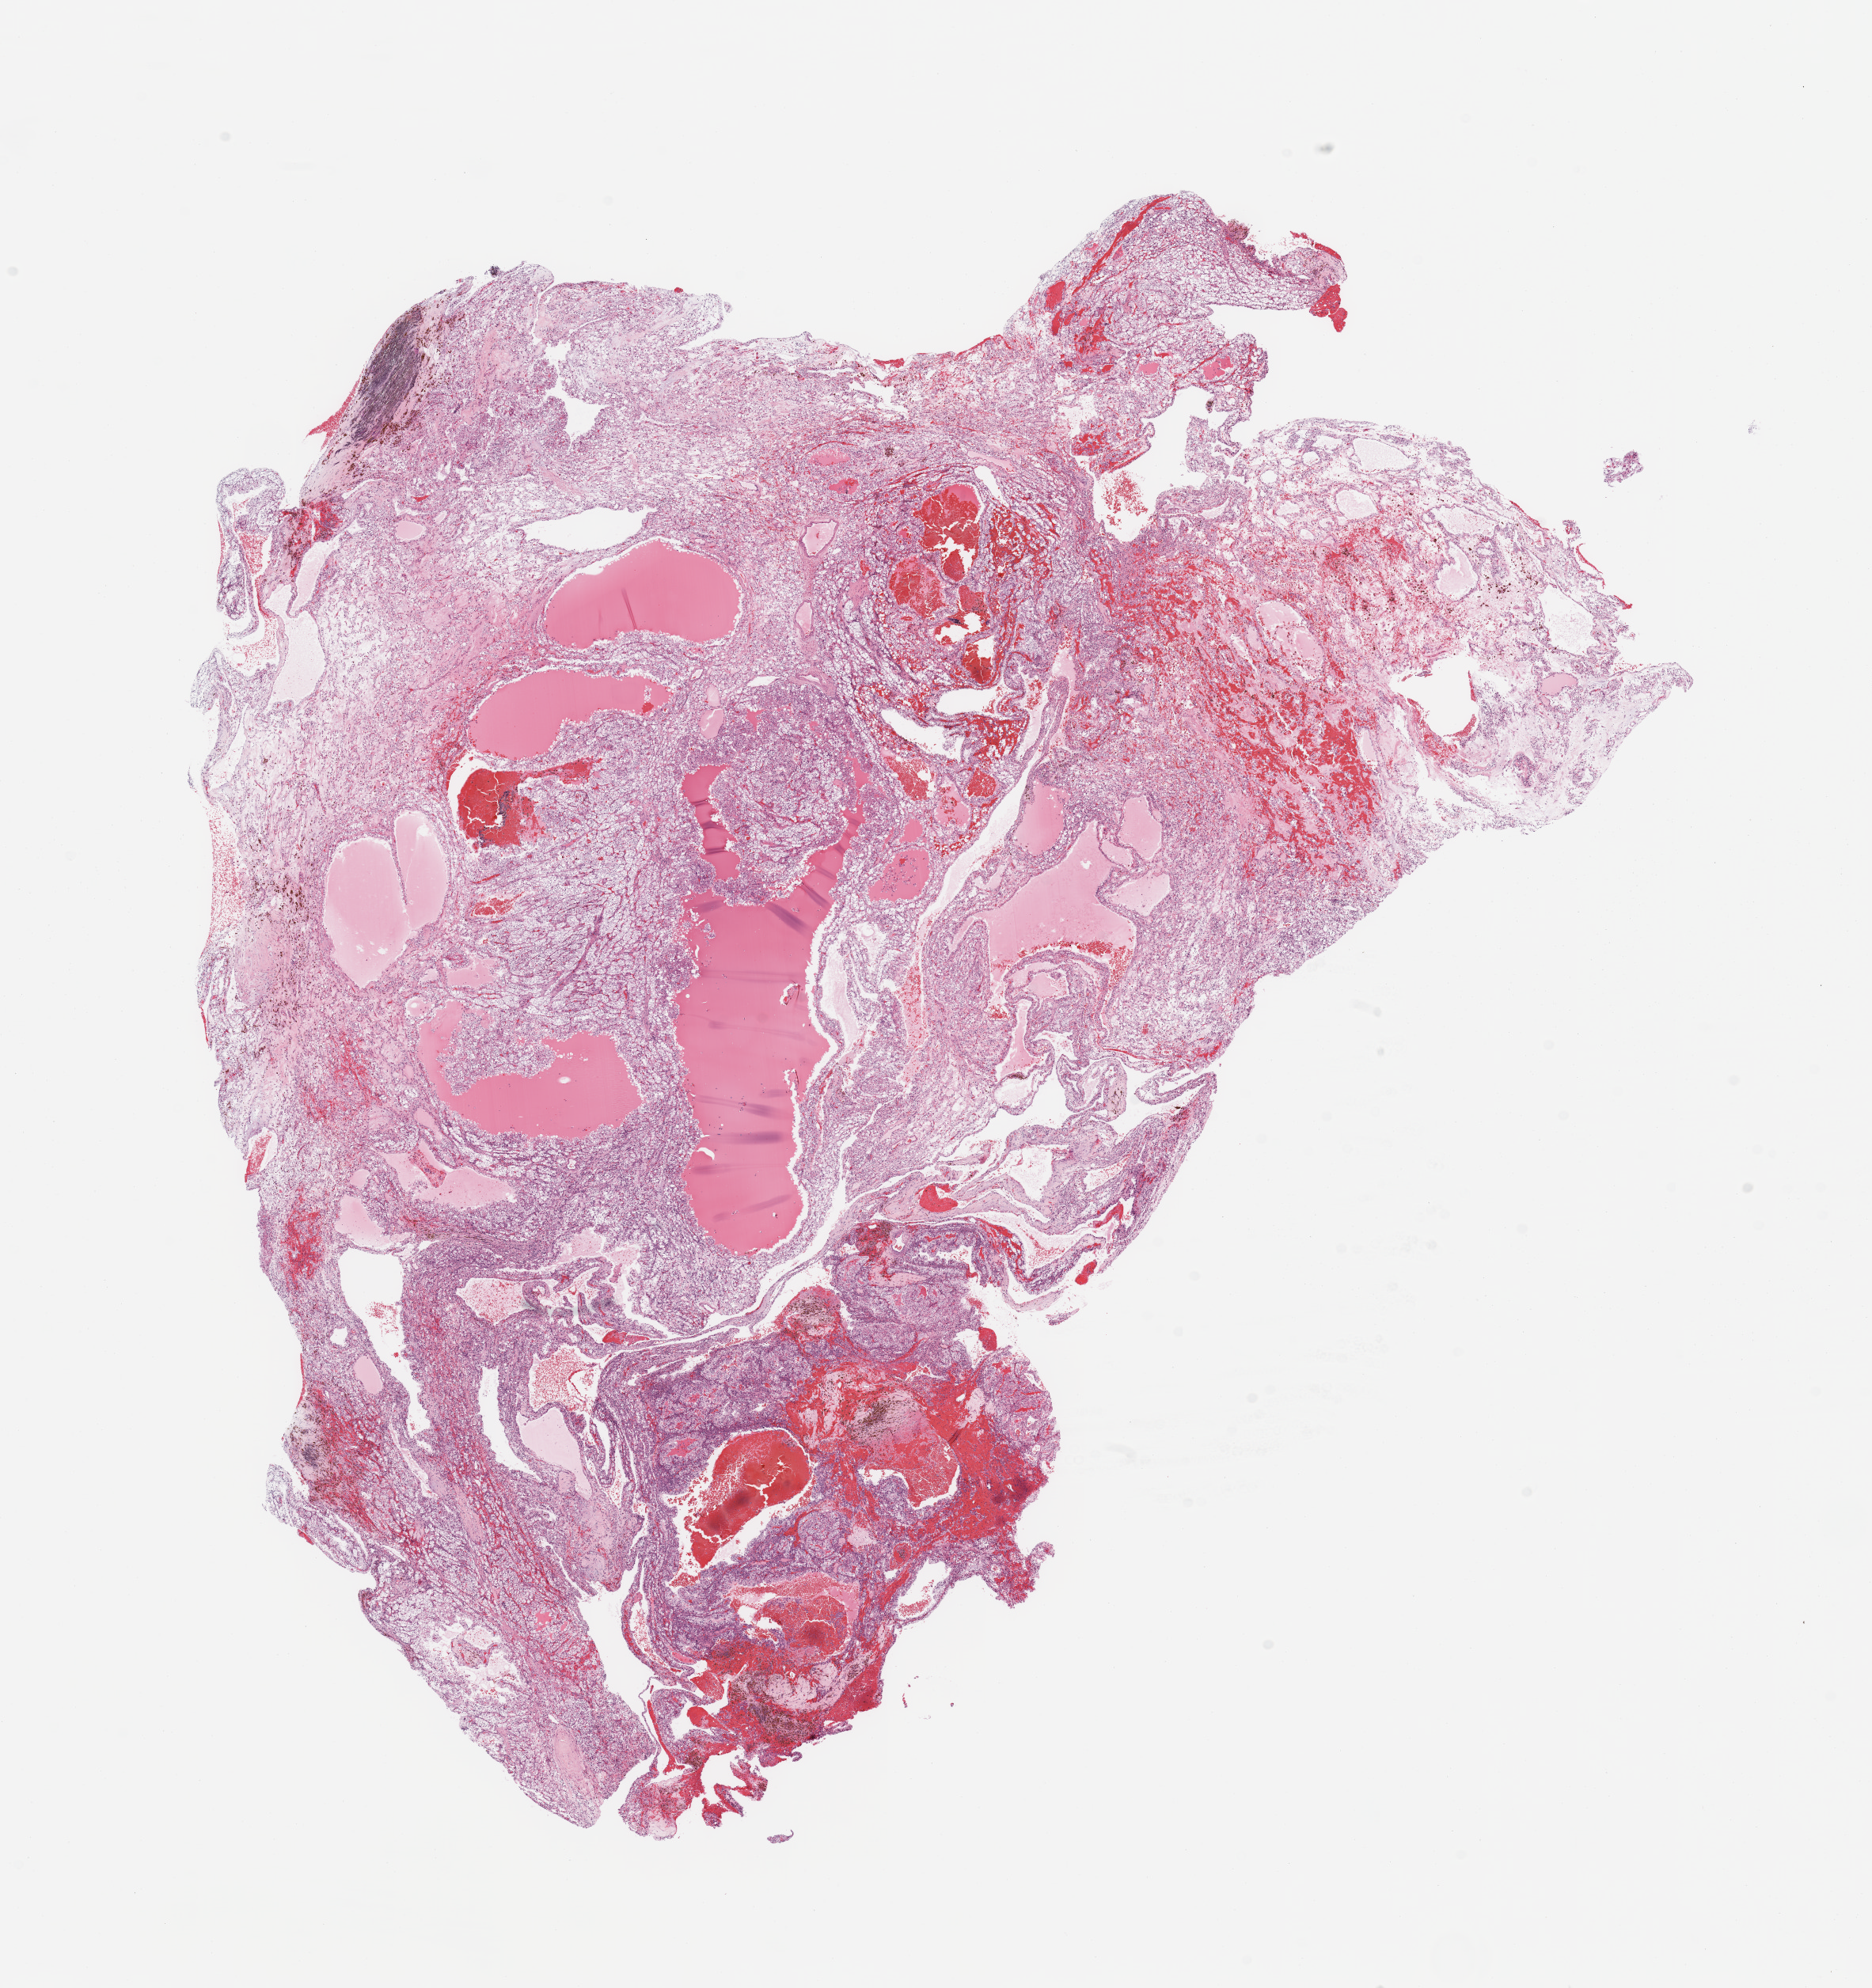
H&E whole-slide image — whole scanned area (about 18.7 x 19.9 mm, from a 20x scan) shown as a low-resolution overview, tumour tissue sample, sampled site: kidney. Patient: male, age 55 years. Histologic grade: G2 (moderately differentiated). Composition of this section per pathologist review: tumour nuclei 85%, necrosis 0%.
Primary tumour site (as recorded): lower pole. AJCC pathologic stage: I. Histologic diagnosis: Renal cell carcinoma, NOS.